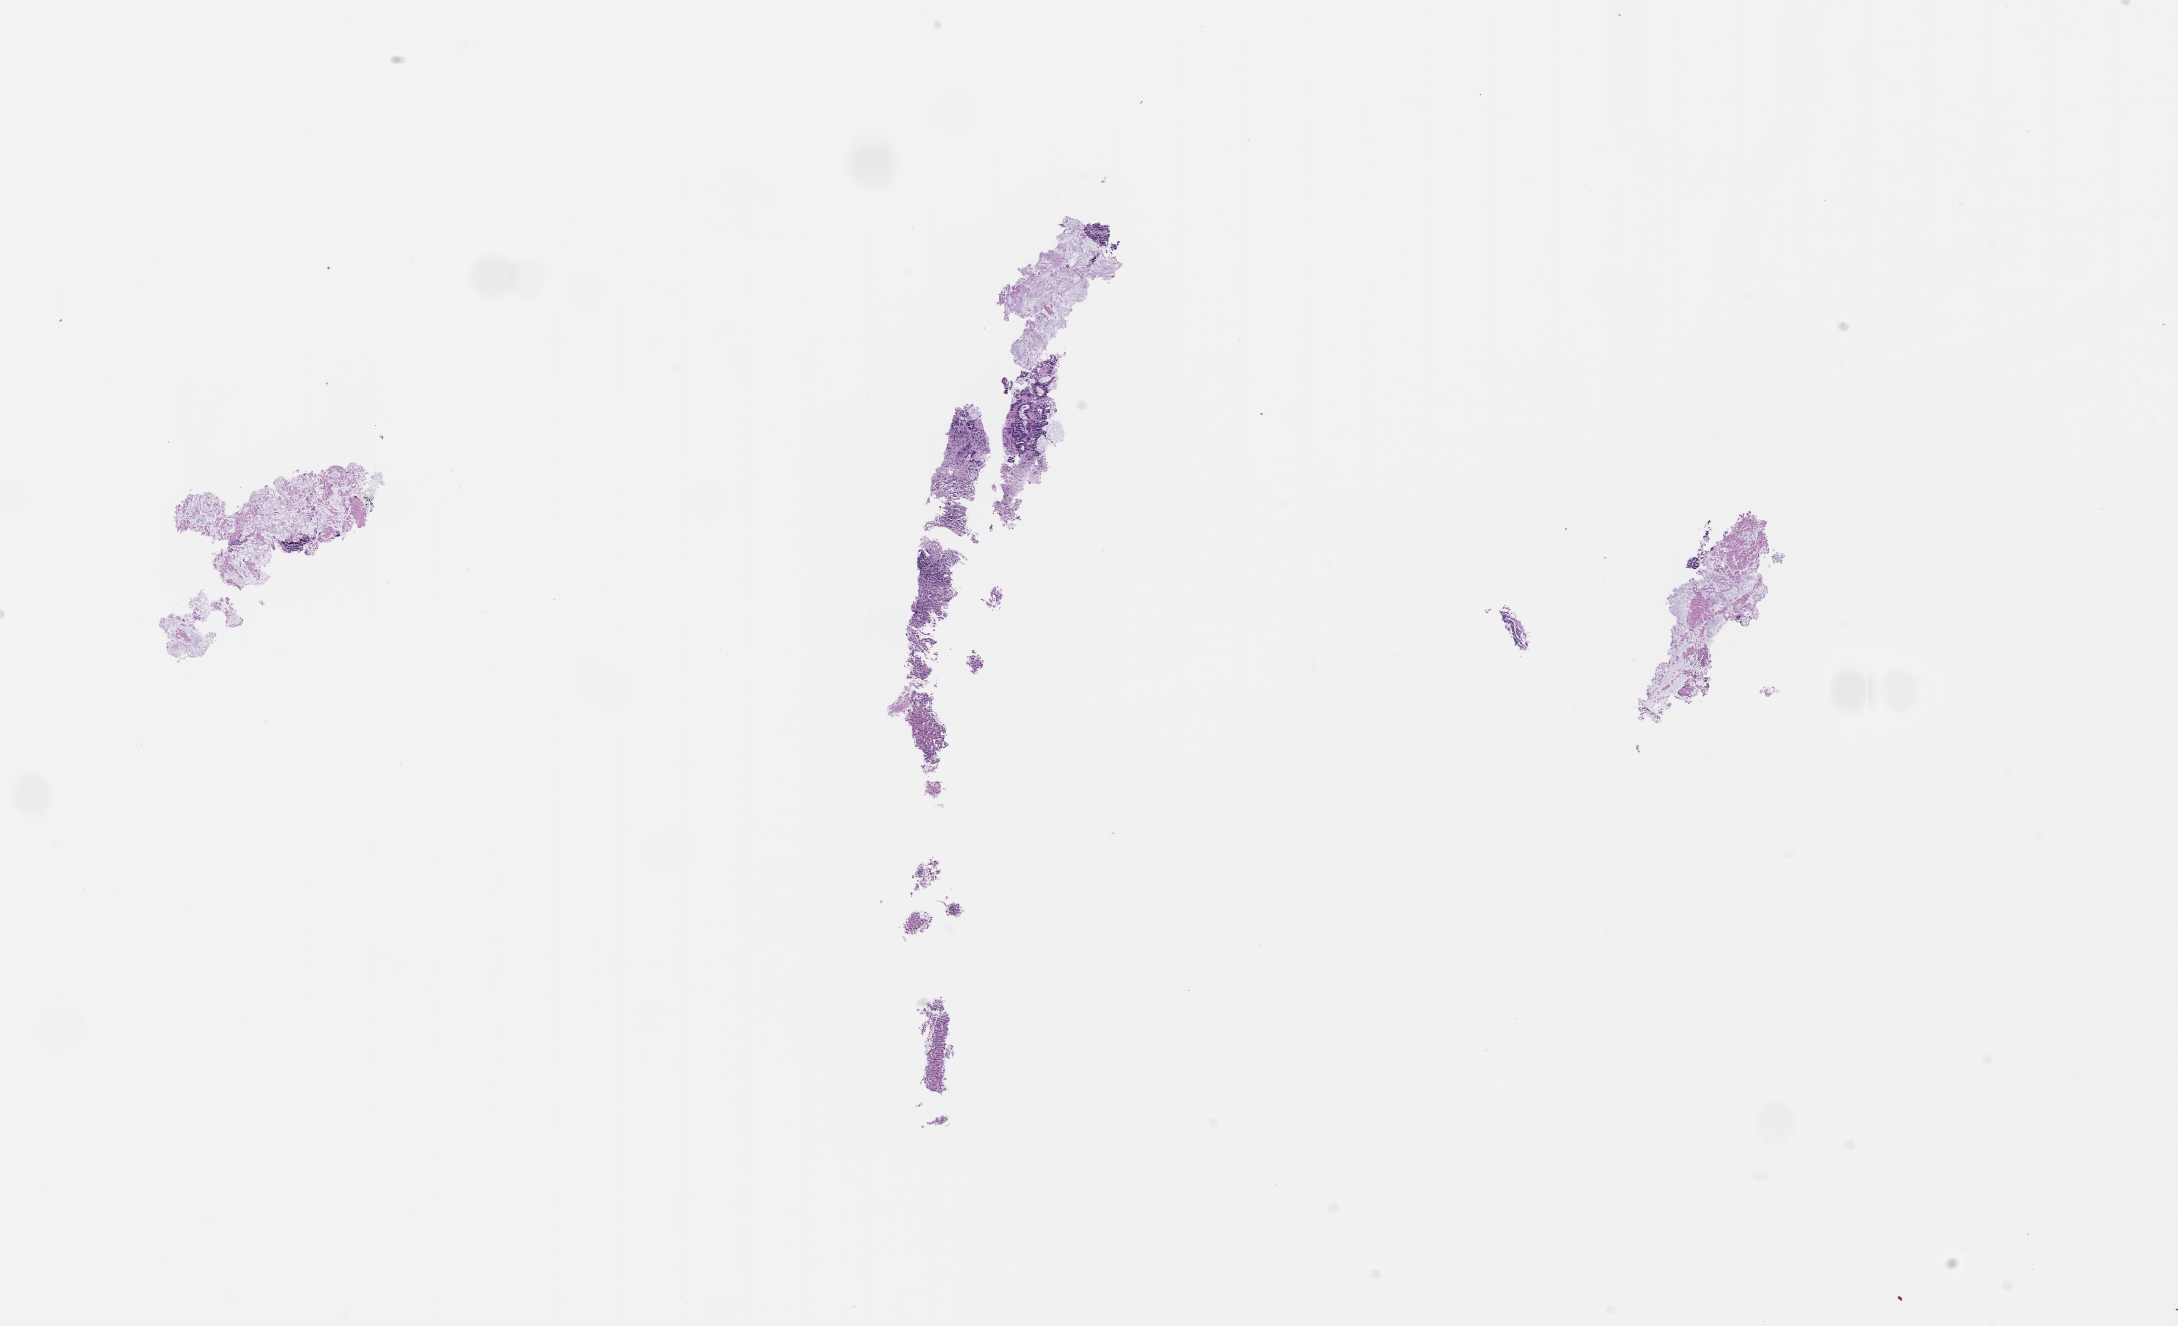
Whole-slide image, hematoxylin and eosin (H&E) stain, whole scanned area (about 17.6 x 10.7 mm) shown as a low-resolution overview, formalin-fixed paraffin-embedded section, collected at baseline (before treatment). Patient sex: female.
• this section: metastasis (sampled organ not recorded)
• patient diagnosis (primary): Colorectal Carcinoma